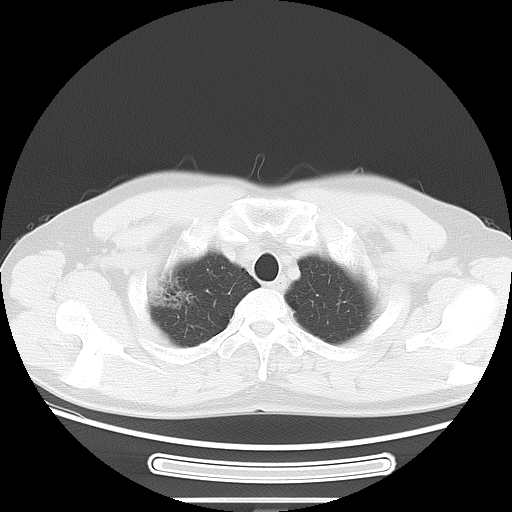
Chest CT, one axial slice. Position 59 of 68 along the scan axis. Reconstruction kernel LUNG. Lung window (W 1500 / L -600 HU). 5 mm slice thickness. 512 × 512 image matrix, field of view 382 × 382 mm. Male patient, age 53 years. Case-level facts recorded for this patient, not image findings: clinical TNM (as recorded): T1c N0 M0; histopathological grade: G2.
Structures marked on this image (bounding box drawn by a radiologist):
- lung tumour (recorded histology: adenocarcinoma): bounding box [x1, y1, x2, y2] px = [143, 268, 199, 316]